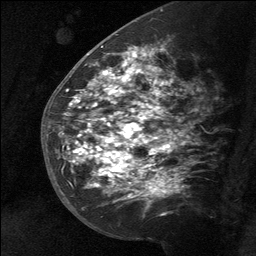
Breast MRI (dynamic contrast-enhanced), one sagittal slice; position 37 of 64 along the scan axis; dynamic contrast-enhanced study with each time point stored as its own series, time point 2 of 3 at this slice position (early post-contrast, ordered by acquisition time); 1.5 T; TE 4.8 ms, TR 27 ms; 2 mm slice thickness; 256 × 256 image matrix, field of view 180 × 180 mm. Female patient, age 39 years. Case-level facts recorded for this patient, not image findings: setting: breast cancer imaged before/during neoadjuvant chemotherapy; receptor status: HER2-positive.
Structures marked on this image (semi-automatically segmented with operator editing):
- analysis volume of interest (the breast-tissue region the enhancement analysis was run in; not a lesion): bounding box [x1, y1, x2, y2] px = [58, 40, 171, 217]
- tumour enhancement mask (voxels above the 90 % enhancement threshold inside the analysis volume of interest): [71, 47, 163, 197]